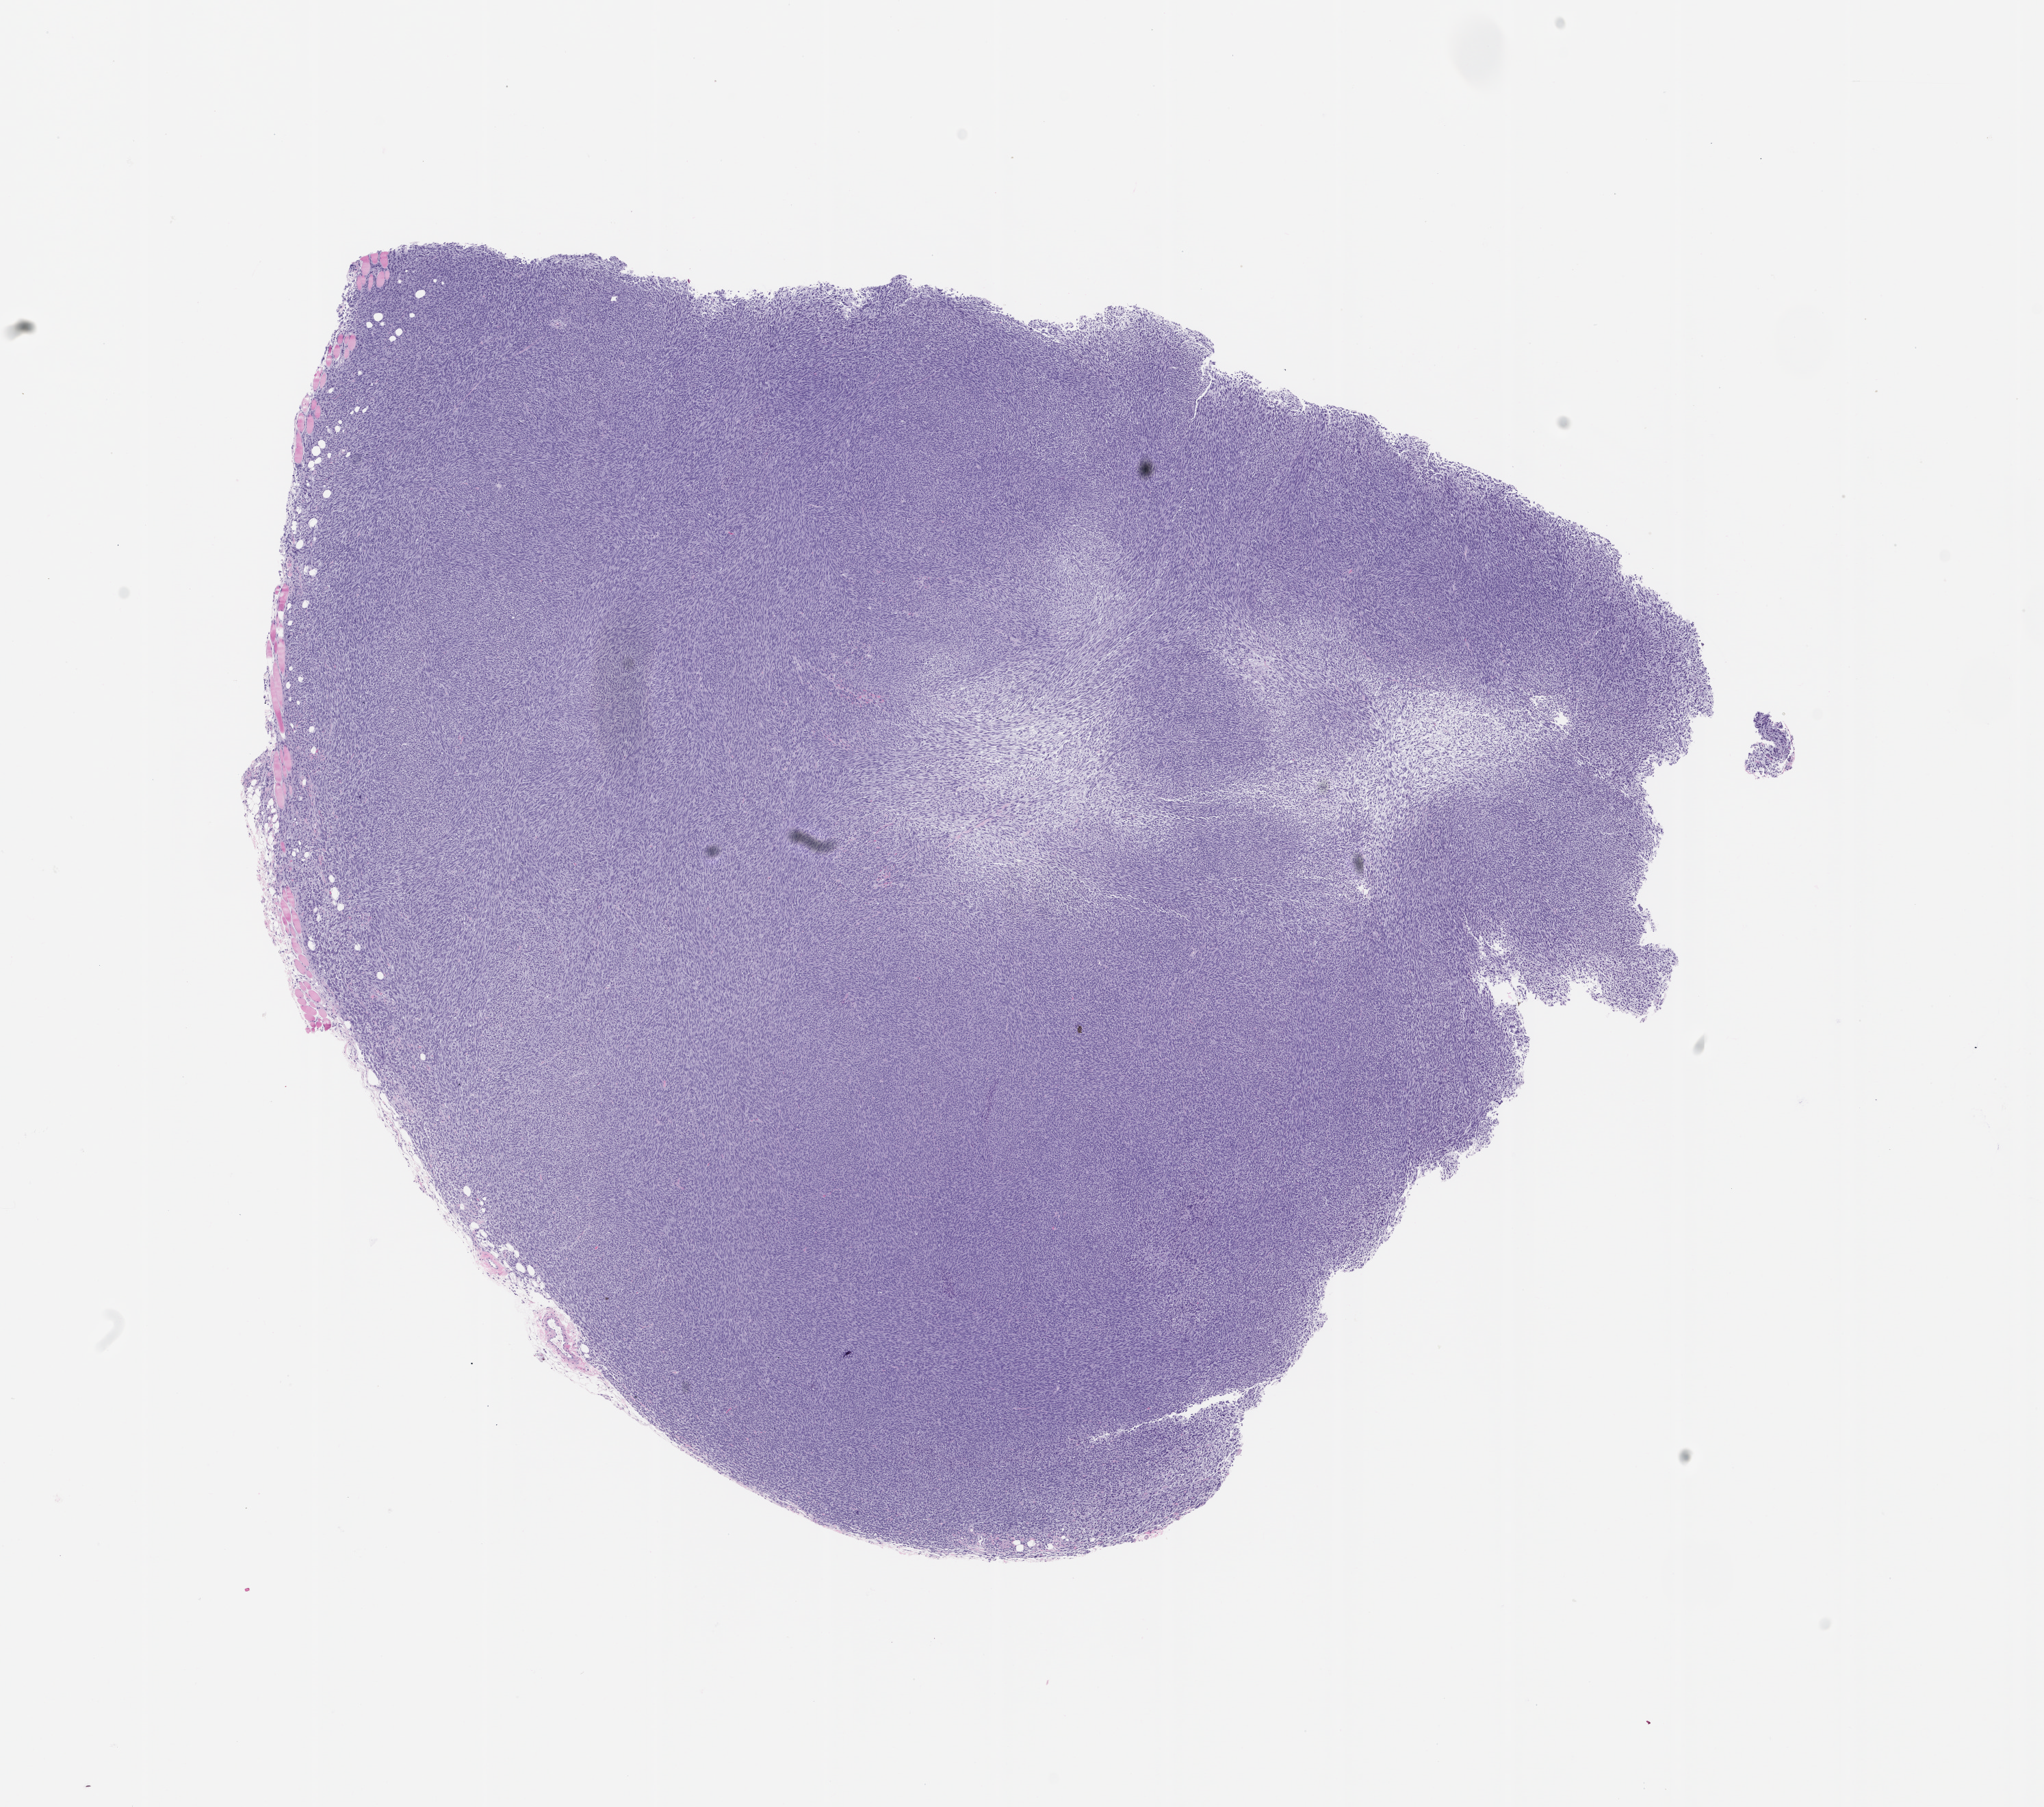
H&E whole-slide image of a patient-derived xenograft (PDX) tumor grown in a mouse, passage 0 — whole scanned area (about 12.0 x 10.6 mm) shown as a low-resolution overview; formalin-fixed, paraffin-embedded (FFPE) tissue; tumor site category: musculoskeletal.
* originating patient diagnosis: Synovial Sarcoma